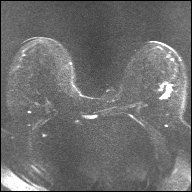
Breast MRI, one axial slice; slice 14 of 32 in the series (ordered by position); diffusion-weighted series; image 2 of 4 stored at this slice position (different b-values; order by instance number); 1.5 T; 4 mm slice thickness; 192 × 192 image matrix. Female patient.
Outlined on this slice (manually delineated by an expert):
- tumour on diffusion-weighted imaging: bounding box [x1, y1, x2, y2] px = [163, 85, 171, 97]